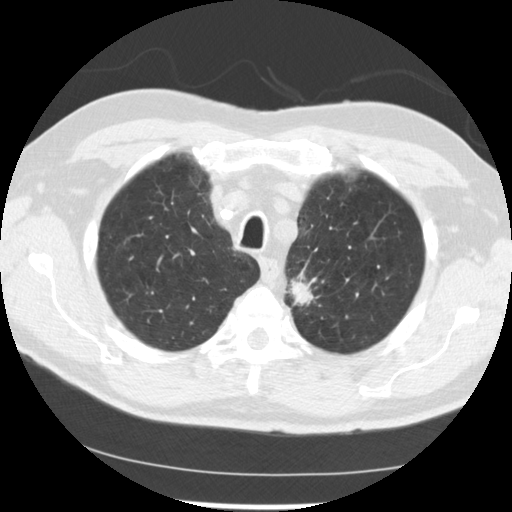
Low-dose screening chest CT, one axial slice. Position 201 of 249 along the scan axis. 120 kVp. Lung window (W 1500 / L -600 HU). 2.5 mm slice thickness. 512 × 512 image matrix, field of view 341 × 341 mm.
Annotated regions visible in this slice (expert manual segmentation):
- lesion 2 (tumor, upper lobe of left lung): bounding box (x1, y1, x2, y2) in pixels: (289, 280, 315, 305)